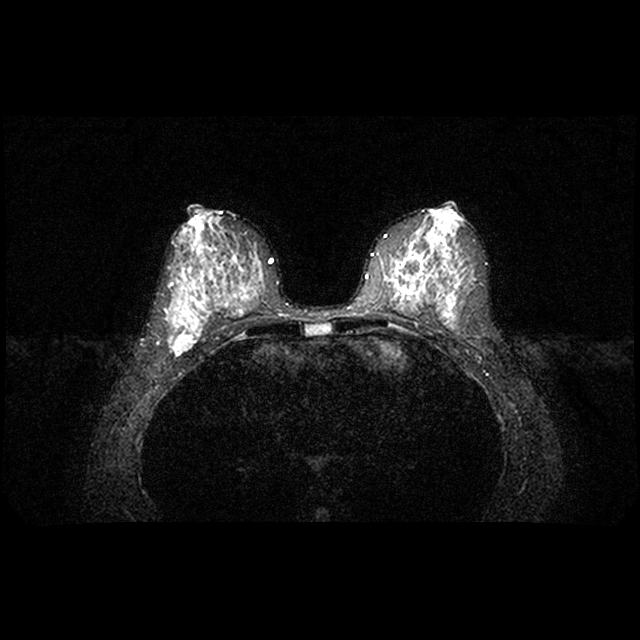
Breast MRI examination; 2 images, each one mid-volume slice chosen by position.
Image 1: axial T2-weighted / STIR image, series "STIR SENSE", slice 44 of 86, 2 mm slice thickness.
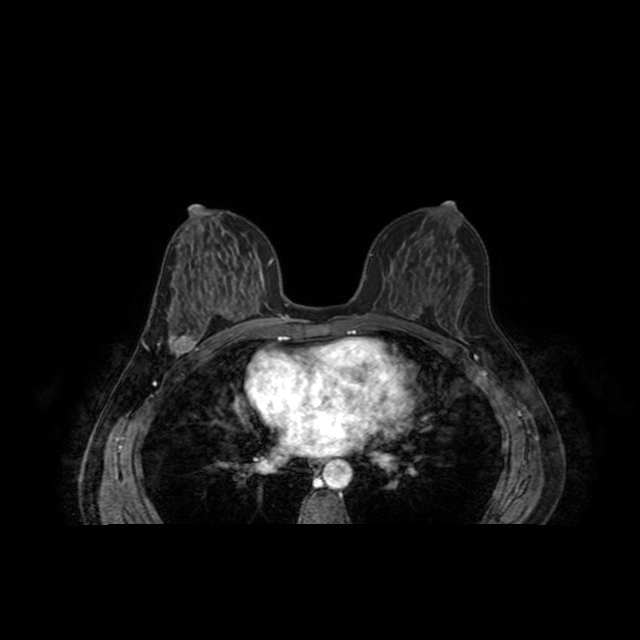
Image 2: axial dynamic contrast-enhanced T1-weighted image, series "AX BLISS_AUTO SENSE", slice 44 of 86, dynamic phase 5 of 8, 4 mm slice thickness.
Patient-level pathology facts (from the clinical record, not from the images): pathology diagnosis: infiltrating ductal CA (right breast); receptor status (as recorded): ER pos (strongly), PR pos (weak), HER2 moderate by fish; pathology report notes: RIGHT BREAST MASS: INFILTRATING DUCTAL CARCINOMA, MODIFIED SCARFF-BLOOM-RICHARDSON GRADE-II/III. A 5% INTRADUCTAL CARCINOMA COMPONENT, COMEDO TYPE, NUCLEAR GRADE III/III, IS ALSO PRESENT.re-bx [date] was no residual tumor.